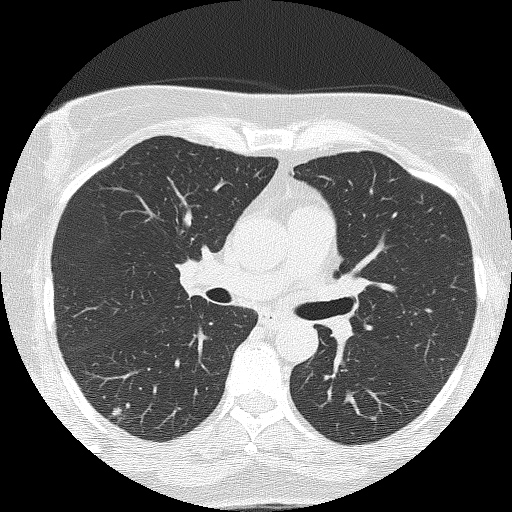
Low-dose screening chest CT, axial slice, second screening round (one year after baseline), lung window (W 1500 / L -600 HU), 2 mm slice thickness, lung (sharp) reconstruction kernel (FC51), slice 62 of 143 in the series. Female participant, aged 58 years at enrolment. Former smoker at enrolment.
Lesion marked by an expert reader, bounding box <83,396,145,438> (left, top, right, bottom; pixels). The screening reader recorded 2 non-calcified nodules or masses ≥4 mm on this exam; which of them this box marks is not recorded. Official screen result: positive, other. Later outcome: lung cancer diagnosed 264 days after this screen — adenocarcinoma, NOS, right lower lobe, well differentiated (G1), stage IB (AJCC 6th edition), 10 mm at pathology.